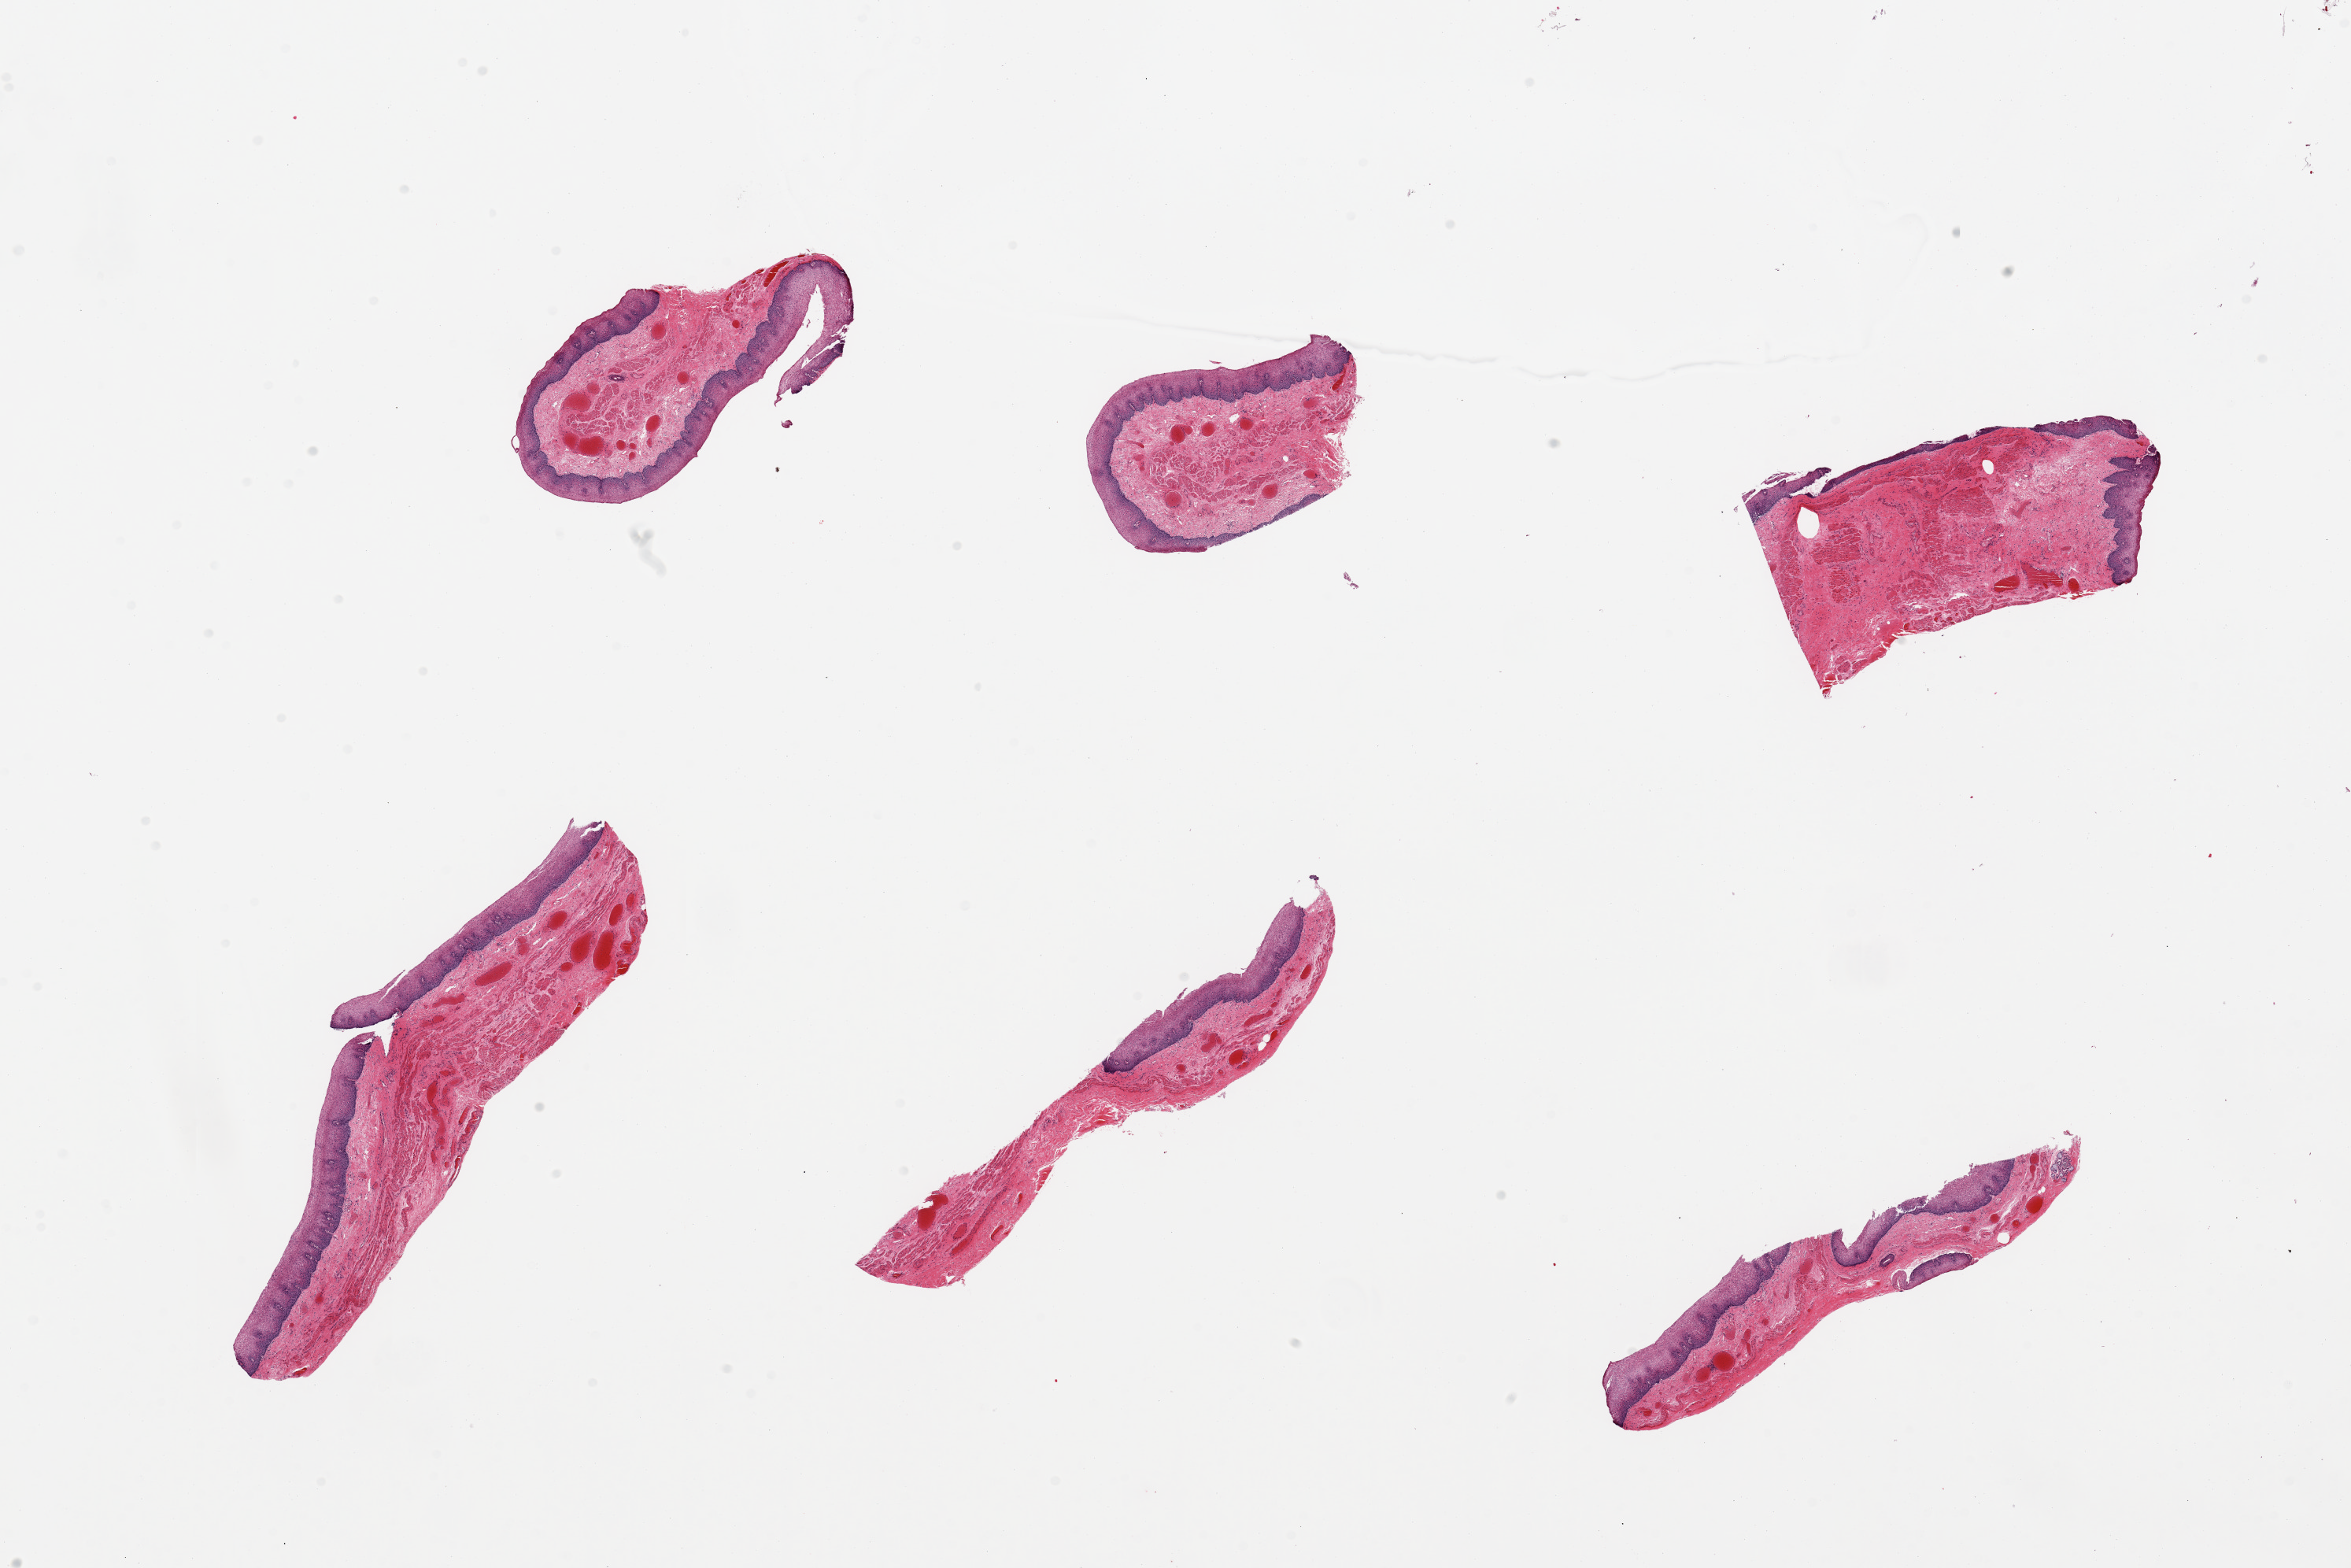
Digitized haematoxylin and eosin-stained section, whole scanned area (about 23.6 x 15.8 mm) shown as a low-resolution overview, PAXgene-fixed paraffin-embedded (PFPE) section, section of esophageal mucous membrane (target tissue), tissue donor sample. Male donor.
Reviewer comment on this tissue sample: 6 pieces; moderate venous congestion.